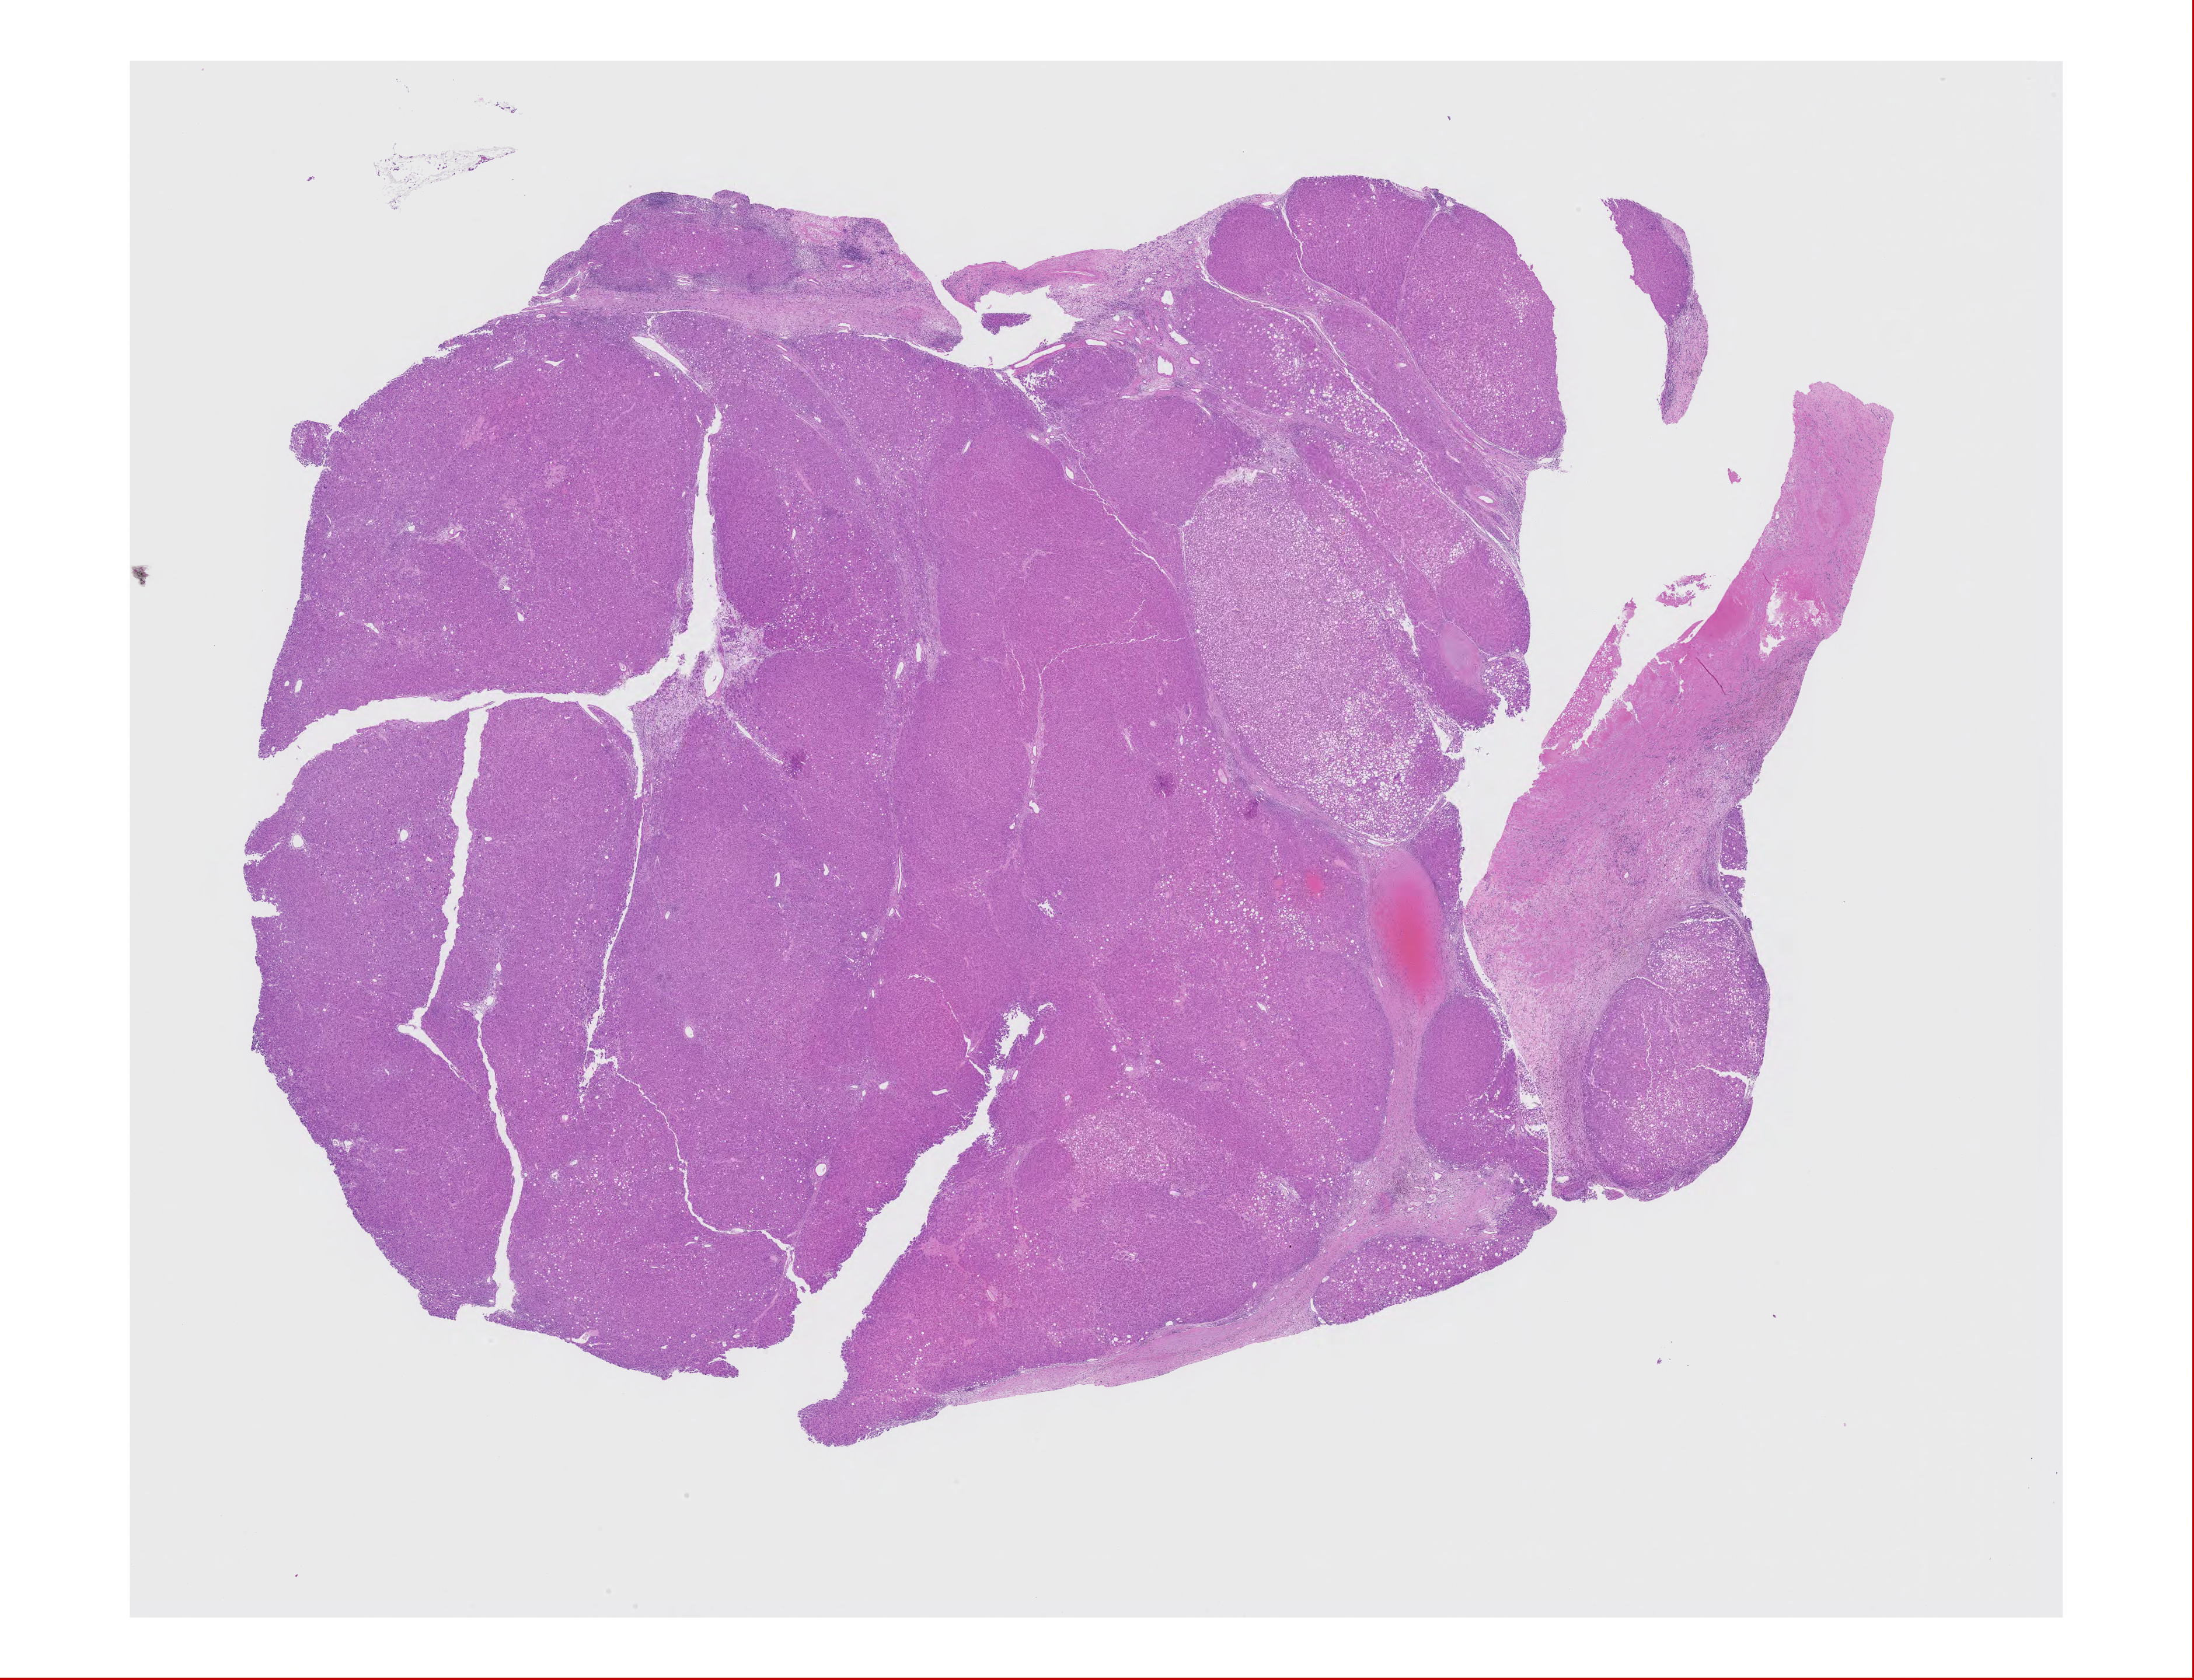
Digitized H&E-stained tissue section (whole slide) — shown as a low-resolution overview of the whole scanned area (about 30.1 x 23.0 mm); formalin-fixed paraffin-embedded (FFPE) diagnostic section; primary tumour sample from the liver. Patient: female, age at initial diagnosis 77 years.
Pathologic diagnosis: Hepatocellular carcinoma, NOS.